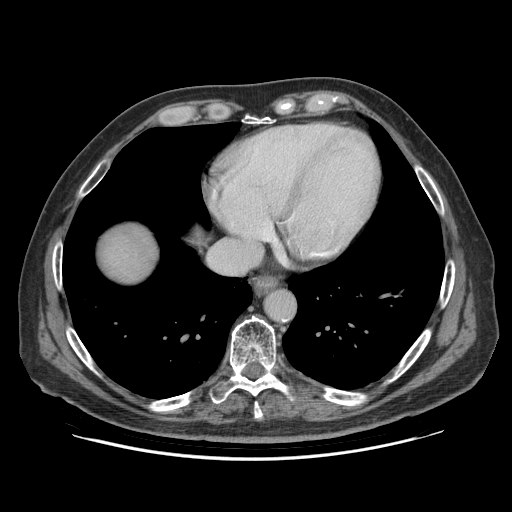
Contrast-enhanced abdominal CT (liver protocol), one axial slice; position 84 of 95 along the scan axis; soft-tissue window (W 400 / L 40 HU); 2.5 mm slice thickness; 512 × 512 image matrix, field of view 400 × 400 mm. From the clinical record (not read from this slice): diagnosis: hepatocellular carcinoma (patient treated with transarterial chemoembolisation; whether this scan precedes or follows treatment is not stated here); TNM stage (as recorded): Stage-IVB.
Outlined on this slice (semi-automatically segmented with operator editing):
- liver parenchyma outside the tumour (the mass and vessels are separate outlines, so this box may not span the whole liver): bounding box <102,228,156,282> (left, top, right, bottom; pixels)